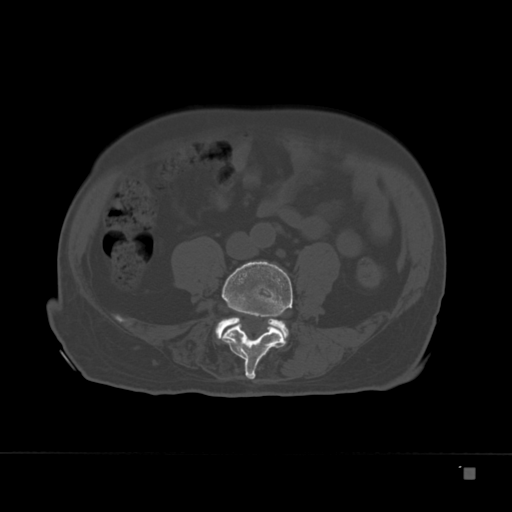
CT including the spine, one axial slice. Position 39 of 332 along the scan axis. 120 kVp. Bone window (W 1800 / L 400 HU). 512 × 512 image matrix. Patient: male, 72 years. From the clinical record (not read from this slice): primary cancer: skeletal.
Outlined on this slice (semi-automatic segmentation, software-assisted and operator-edited):
- L4 vertebra: bounding box [x1, y1, x2, y2] px = [223, 261, 293, 381]
- L5 vertebra: [215, 317, 290, 339]